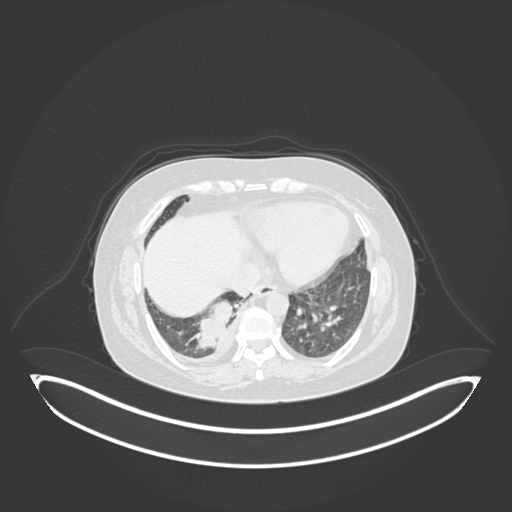
Chest CT, one axial slice; slice 39 of 231 in the series (ordered by position); reconstruction kernel B30f; lung window (W 1500 / L -600 HU); 1 mm slice thickness; 512 × 512 image matrix, field of view 500 × 500 mm. Female patient, age 56 years. Case-level facts recorded for this patient, not image findings: clinical TNM (as recorded): T2b N1 M0; histopathological grade: G3.
Structures marked on this image (rectangle marked by the reading radiologist):
- lung tumour (recorded histology: small cell carcinoma): box from (x=185, y=289) to (x=238, y=354) px